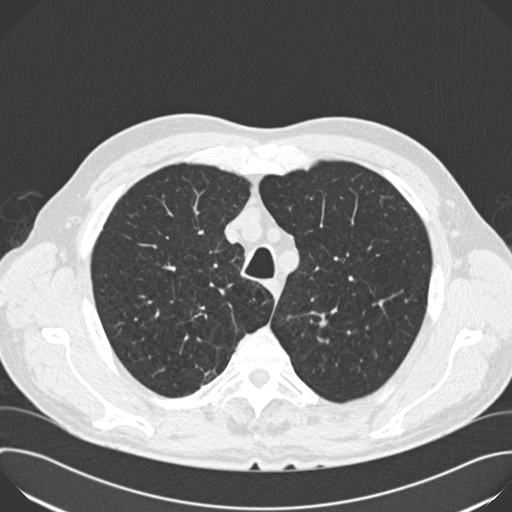
Axial slice from a low-dose chest CT screening exam; second screening round (one year after baseline); lung window (W 1500 / L -600 HU); 2 mm slice thickness; standard (soft-tissue) reconstruction kernel (B30f); 512 × 512 image matrix. Male, age 66 years at enrolment.
Expert-annotated lung lesion, box from (x=304, y=303) to (x=343, y=342) px. Screening reader's record for this exam (one nodule recorded; not confirmed to be the boxed lesion): non-calcified nodule or mass ≥4 mm, left upper lobe, 8 × 7 mm, poorly defined margins, soft tissue attenuation, pre-existing on the prior screen: yes; interval growth: yes. Official screen result: positive, other. Later outcome: lung cancer diagnosed 390 days after this screen (after the third annual screen) — squamous cell carcinoma, NOS, left upper lobe, poorly differentiated (G3), stage IA (AJCC 6th edition), 15 mm at pathology.